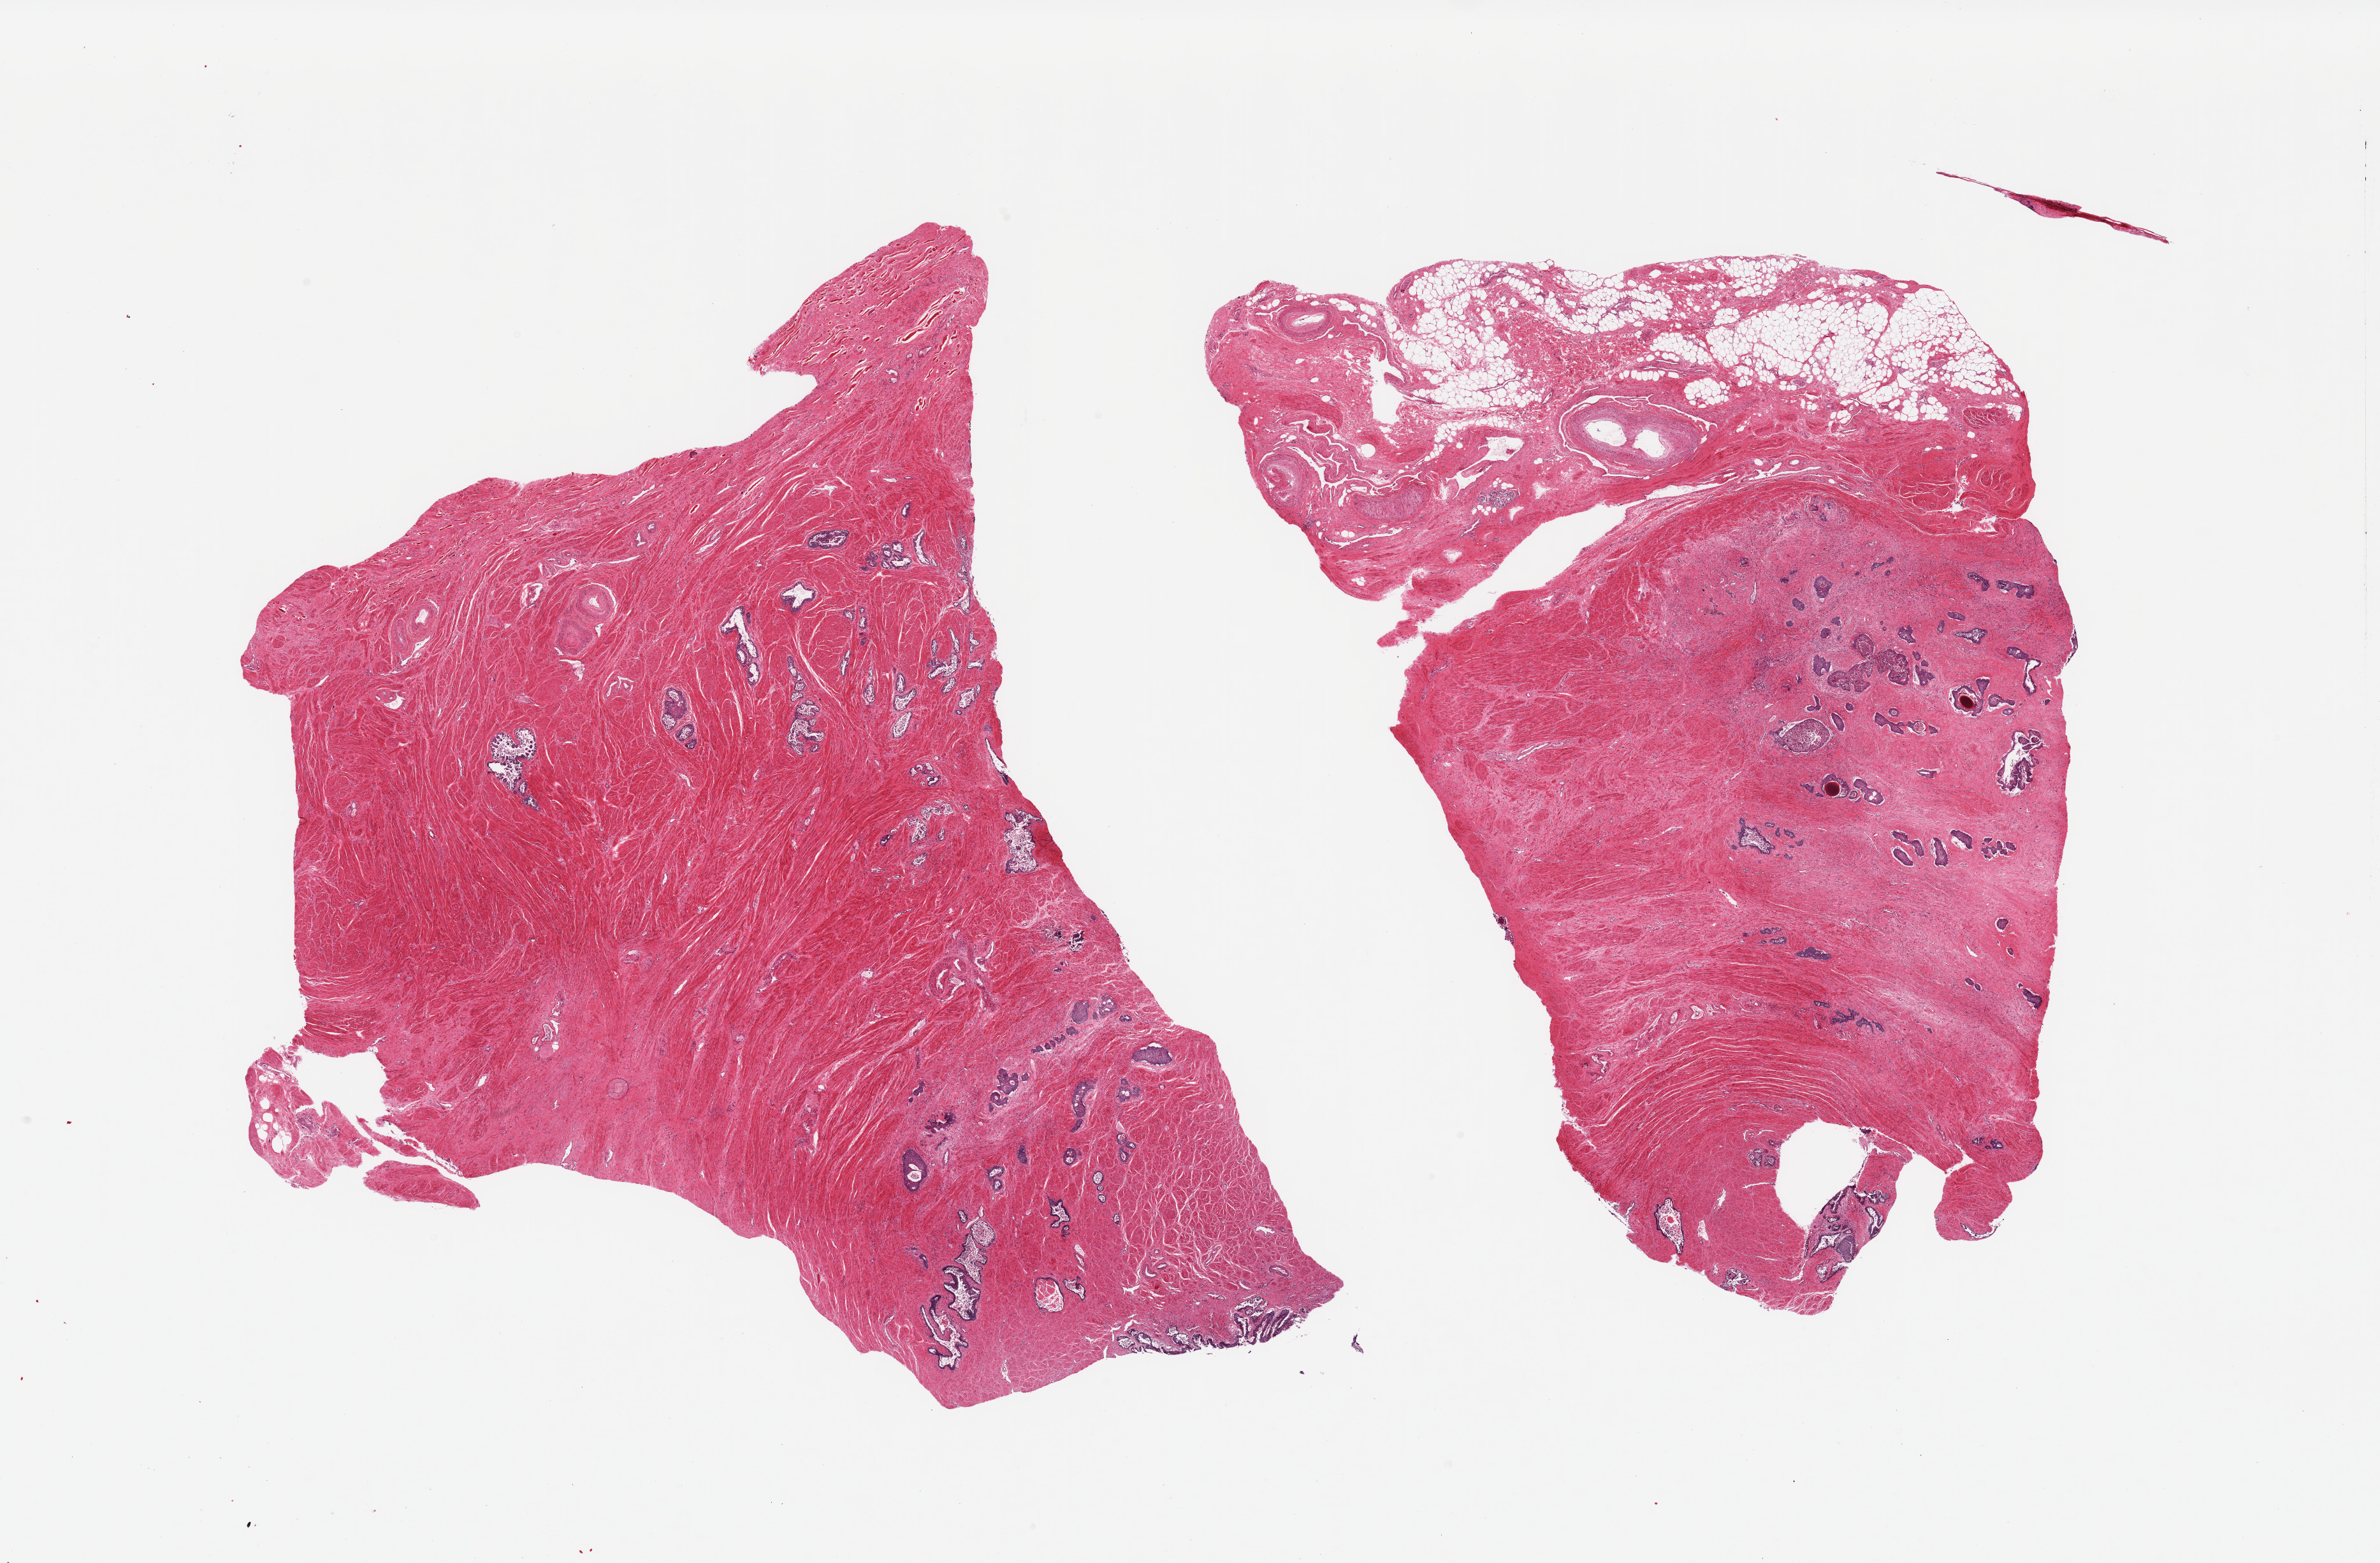
Digitized hematoxylin and eosin (H&E)-stained section, a low-resolution overview of the entire scanned area, about 29.5 x 19.4 mm; PAXgene-fixed, paraffin-embedded tissue; section of prostate (target tissue); donor tissue sample. Donor: male.
Reviewer comment on this tissue sample: 2 pieces; stroma predominates (90%) over glands; glands autolyzed, stroma intact; 3.5mm 'cap' of fibroadipose vascularized tissue at end of 1 piece.